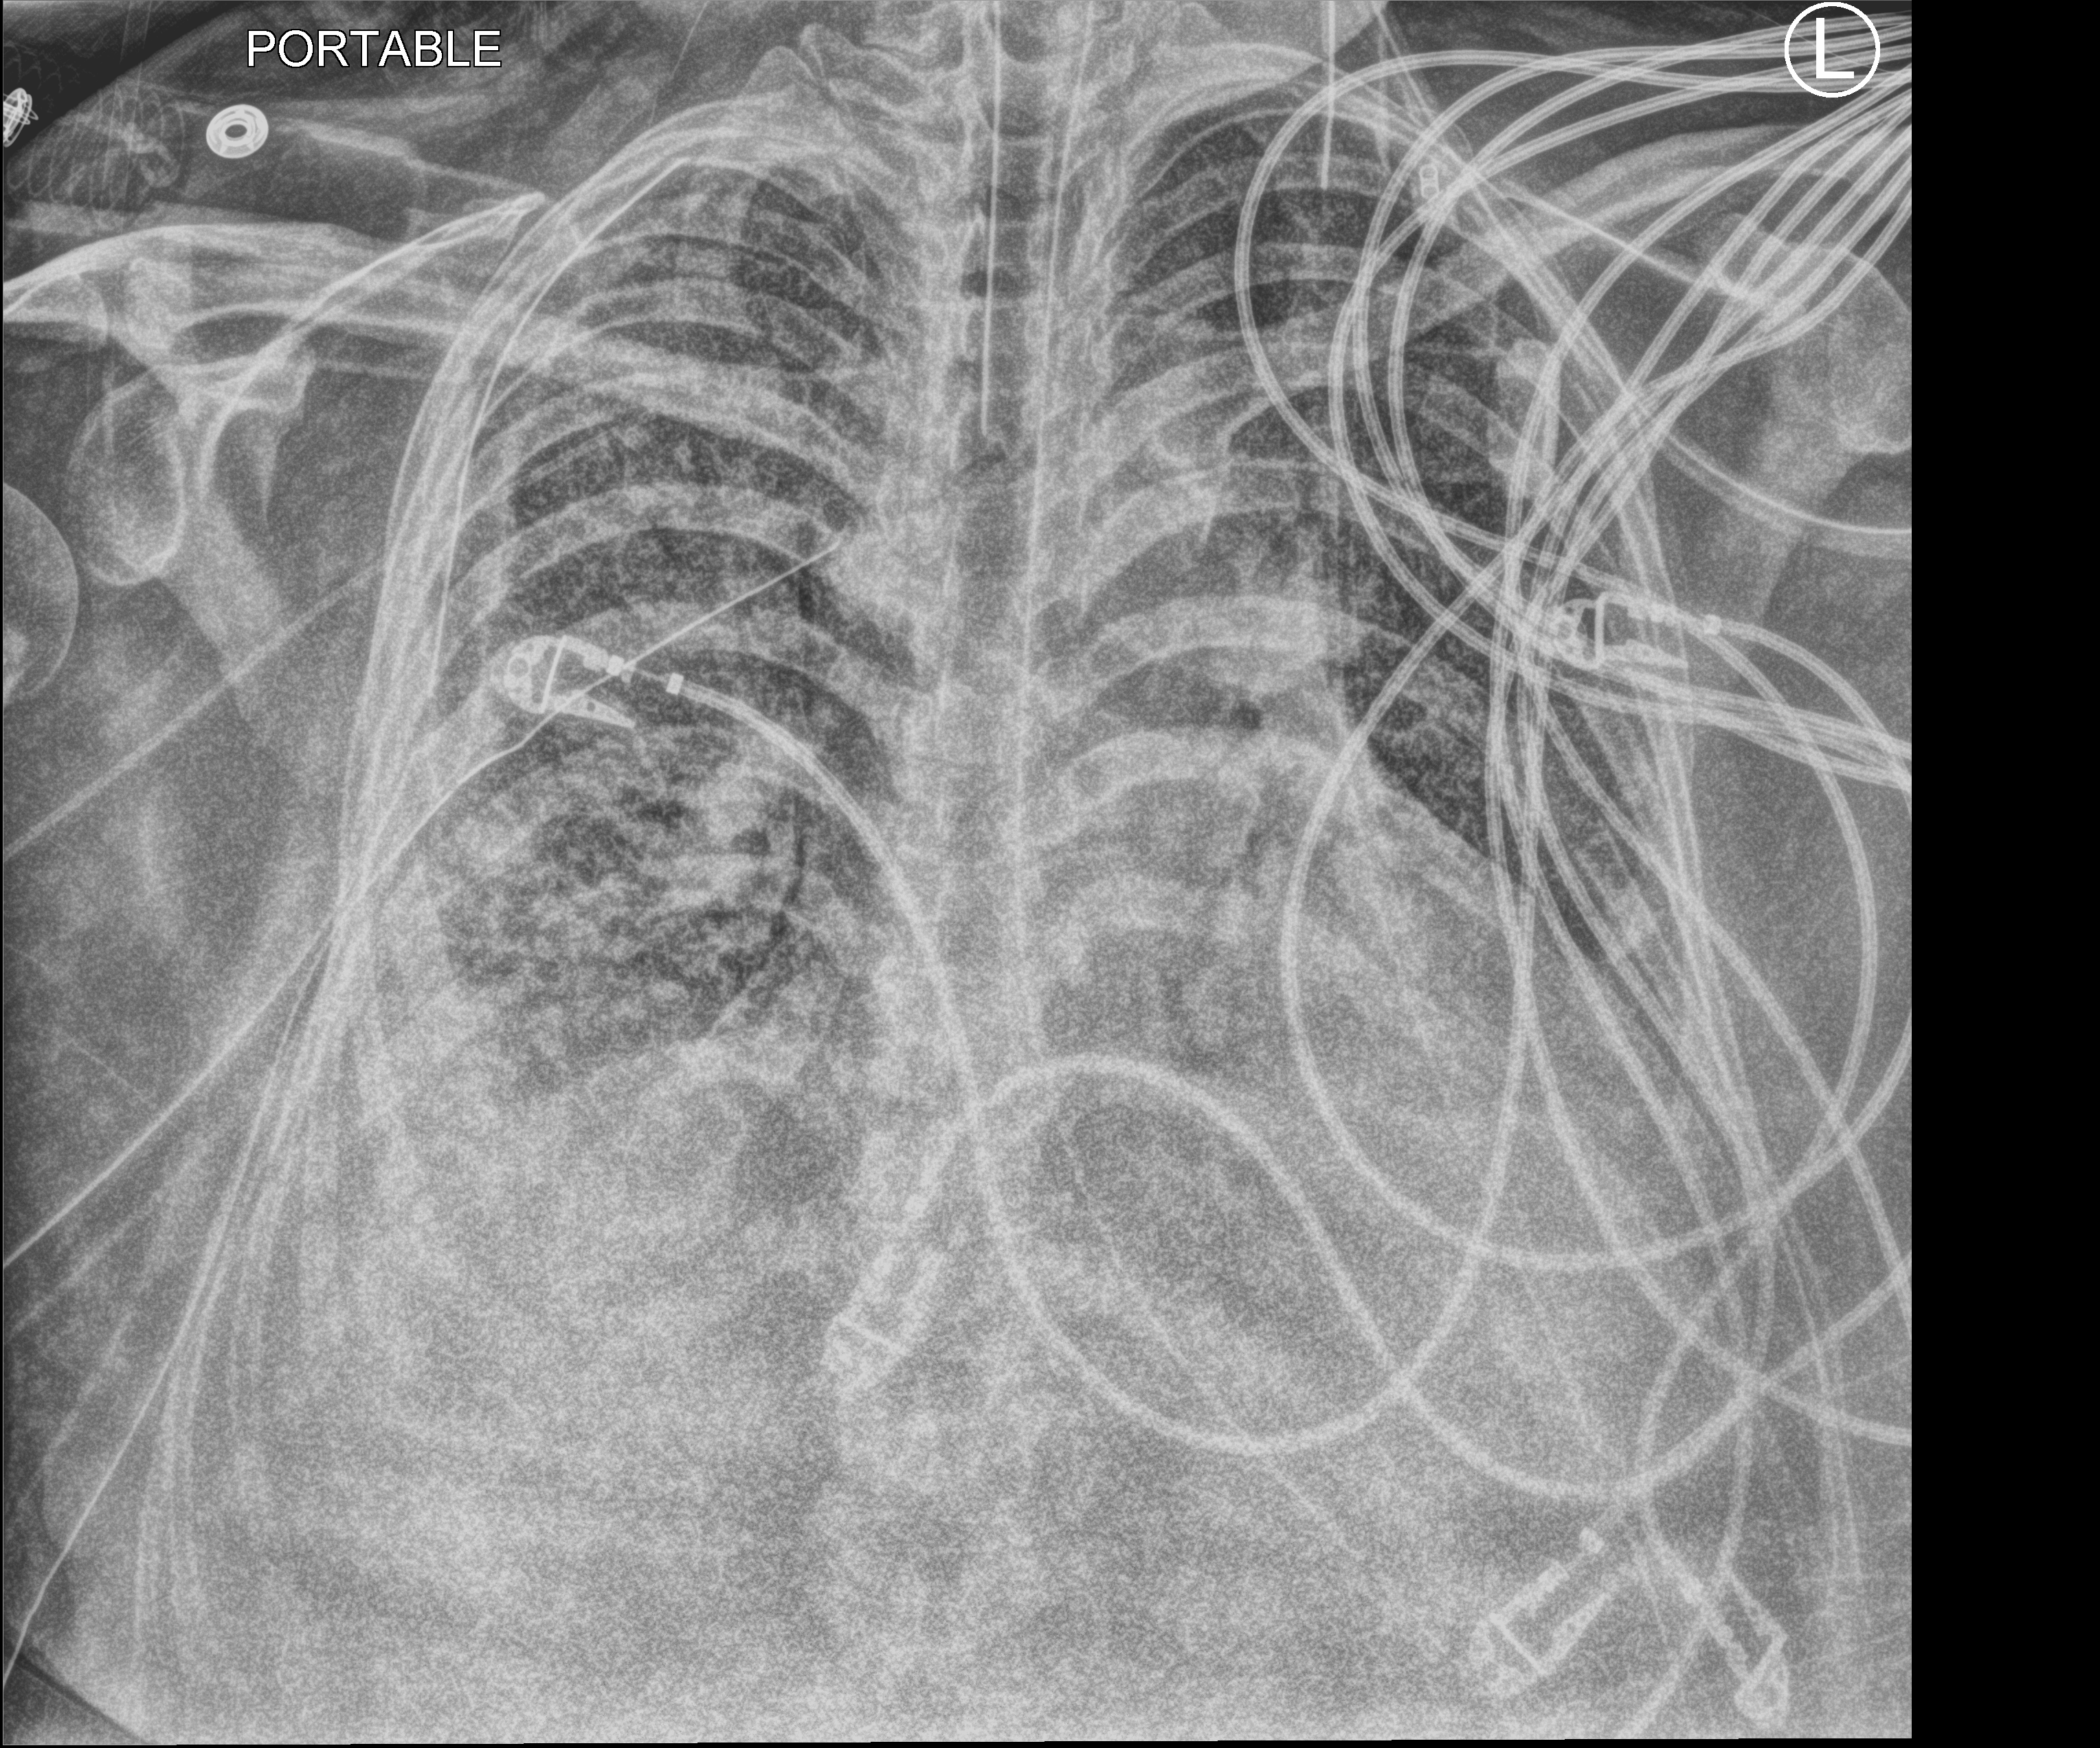
Portable chest radiograph, anteroposterior (AP) projection. Adult patient hospitalised with COVID-19, age 18–59 years.
Admission-level facts for this patient (not findings on this image; timing relative to this image not recorded):
- smoking status (admission record): never